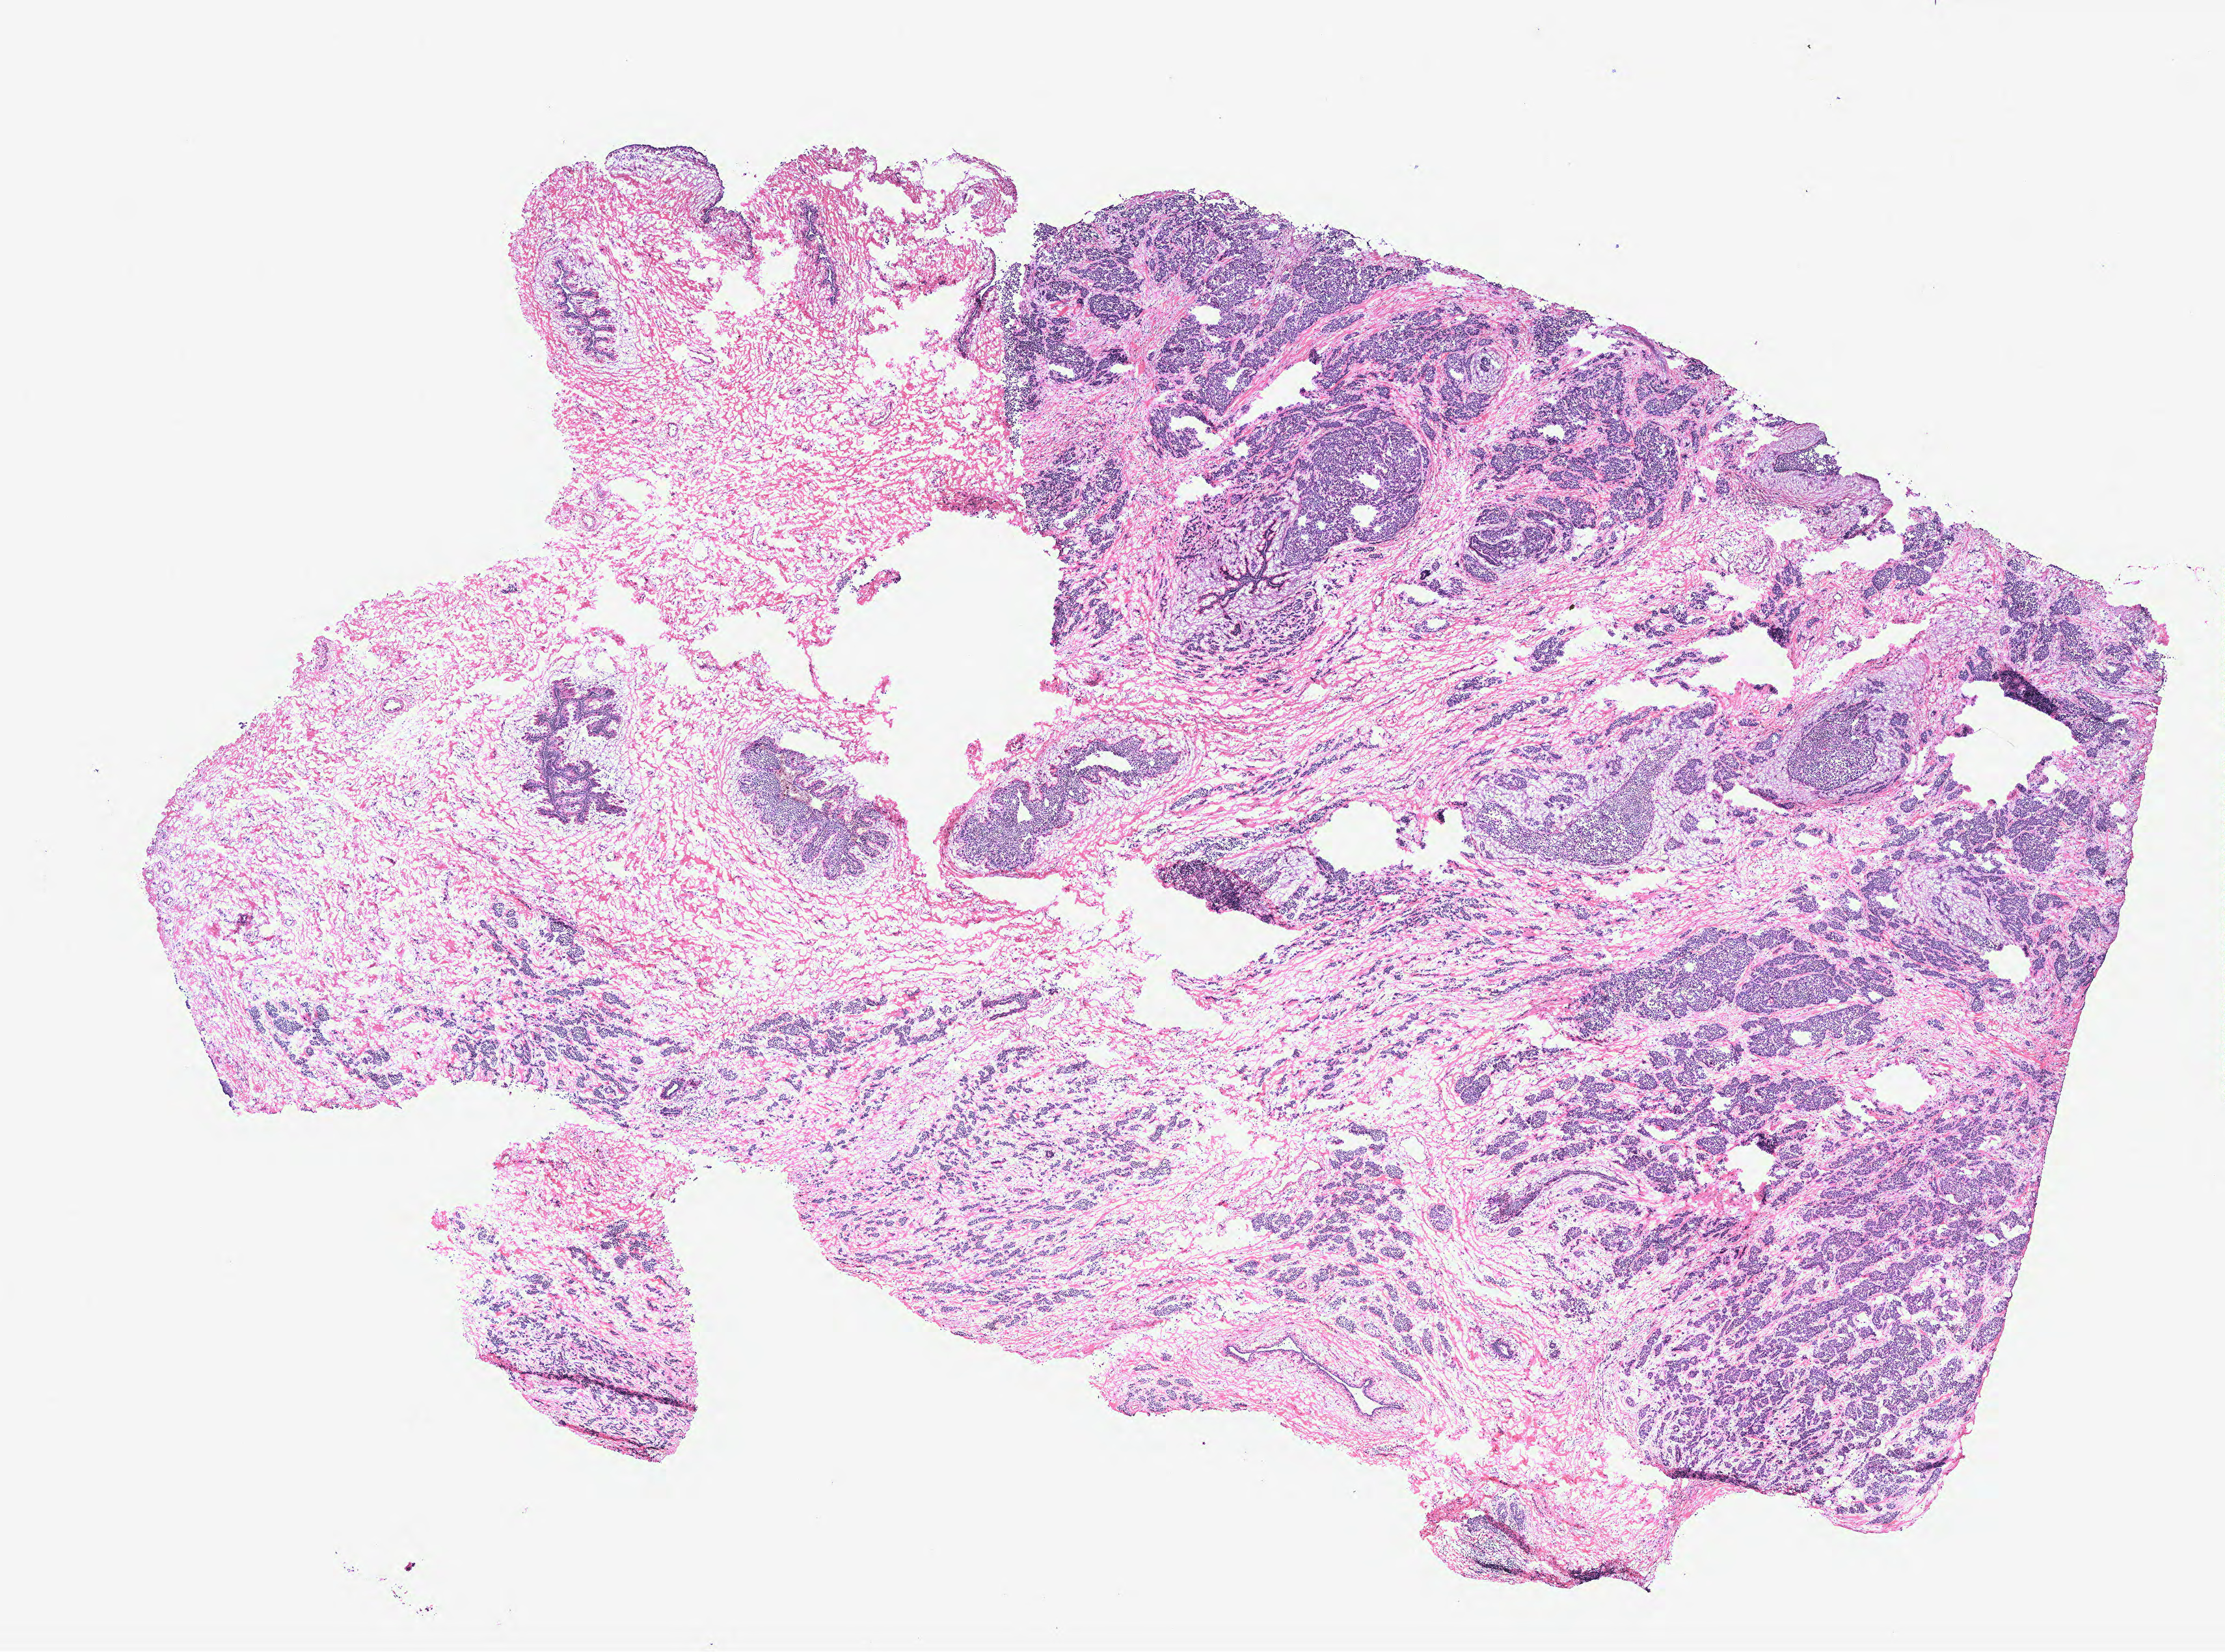
Hematoxylin and eosin (H&E) stained whole-slide image — shown as a low-resolution overview of the whole scanned area (about 13.7 x 10.2 mm, from a 40x scan); breast, tissue type not recorded. Female, 67 y/o.
• patient diagnosis: Infiltrating duct carcinoma, NOS